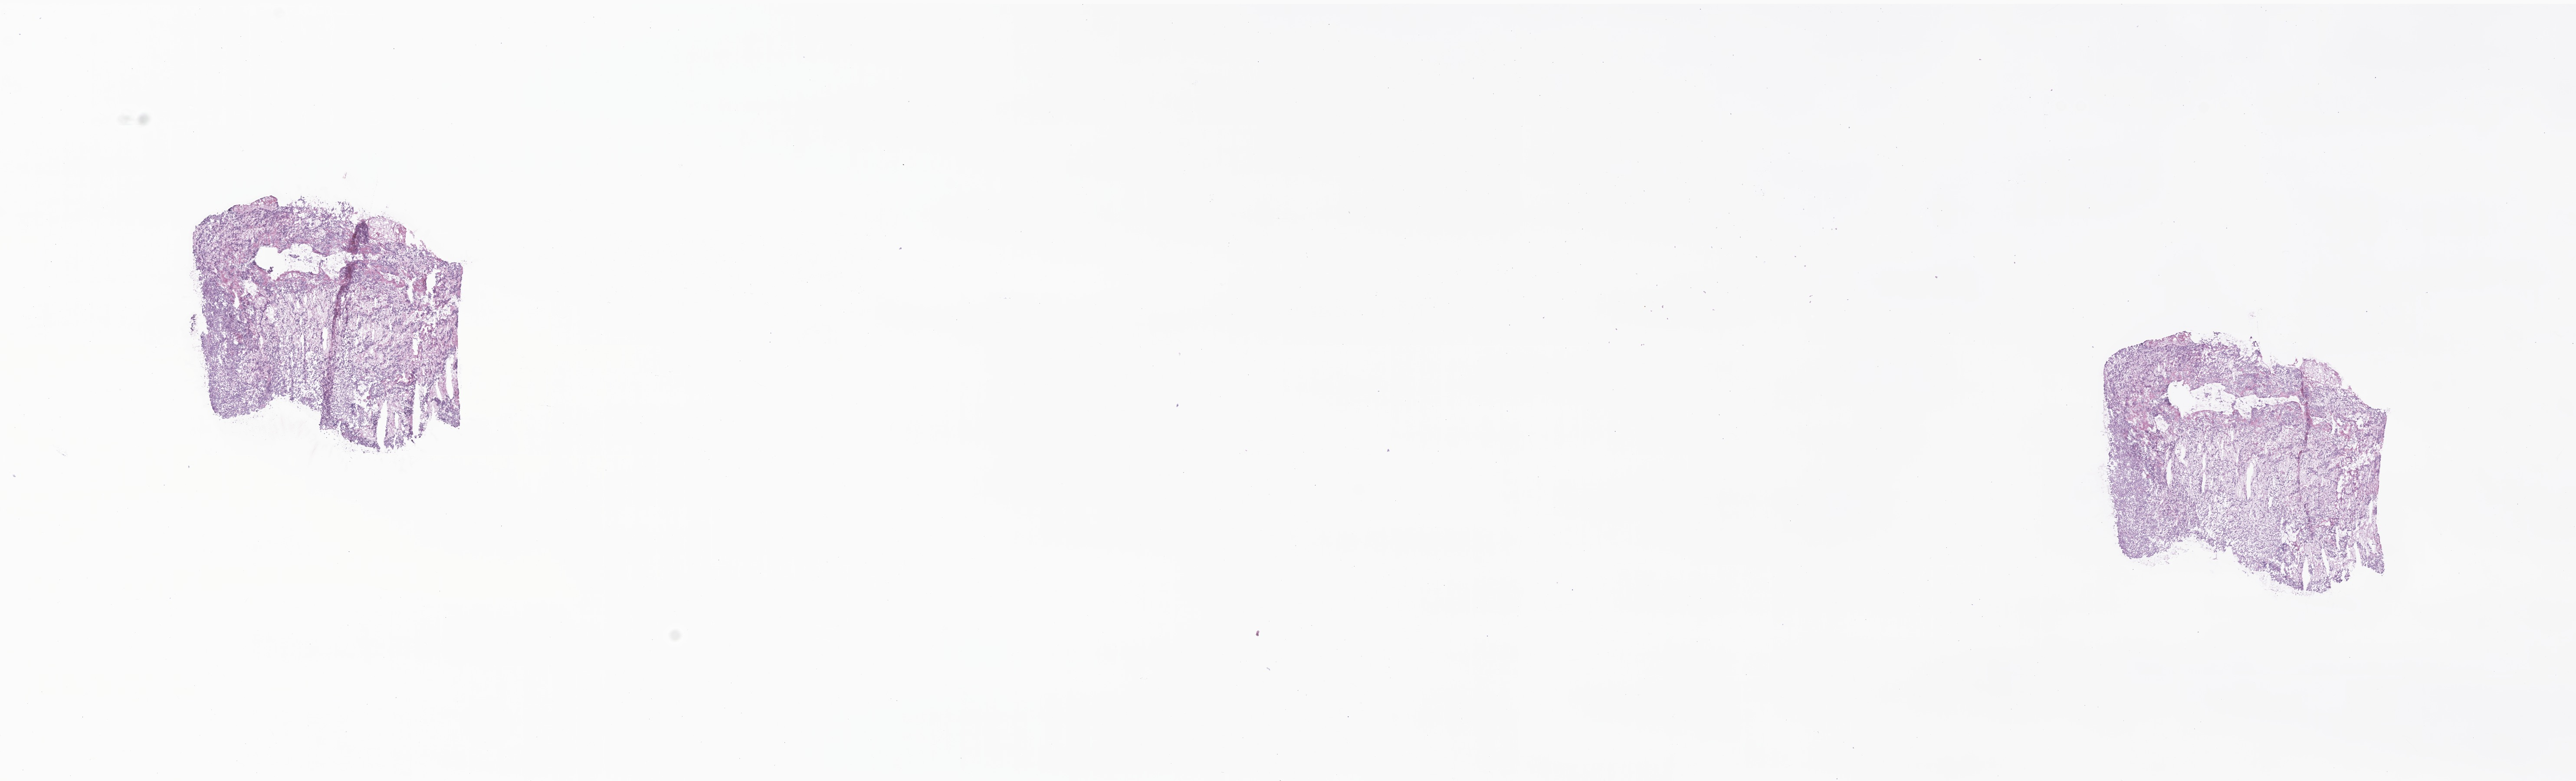
Digitized H&E-stained section of tumor tissue from the brain, a low-resolution overview of the entire scanned area, about 25.0 x 7.6 mm, frozen section. Patient: female, age 121 months (10 years 1 month).
* diagnosis: Medulloblastoma, NOS